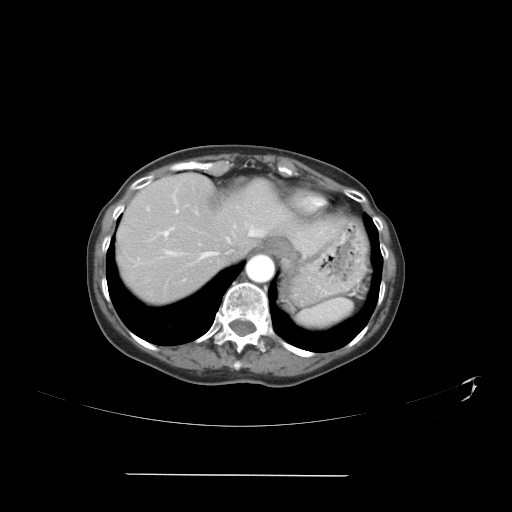
Contrast-enhanced abdominal CT, one axial slice; slice 32 of 41 in the series (ordered by position); 120 kVp; intravenous contrast given; soft-tissue window (W 400 / L 40 HU); 512 × 512 image matrix, field of view 431 × 431 mm. Female patient, age 74 years. Case-level facts recorded for this patient, not image findings: diagnosis: colorectal cancer liver metastases, imaged before liver resection; multiple liver metastases: yes; largest metastasis: 3.3 cm; disease in both lobes: yes.
Structures marked on this image (manually delineated by an expert):
- hepatic veins: bounding box <160,210,275,262> (left, top, right, bottom; pixels)
- liver: <118,174,332,301>
- planned liver remnant (the part of the liver to remain after resection): <121,174,333,258>
- portal vein (with intrahepatic branches): <162,210,179,236>